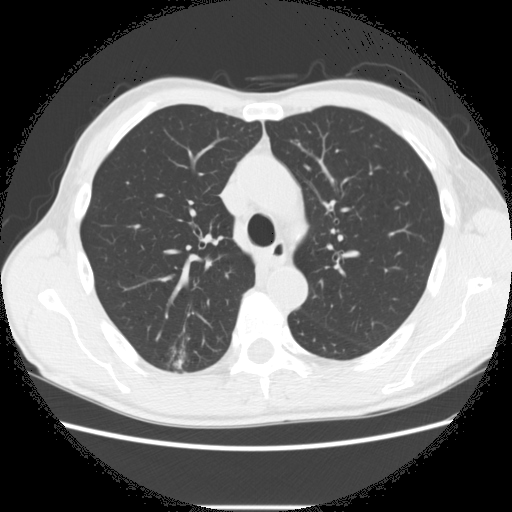
Low-dose screening chest CT, one axial slice. Position 197 of 282 along the scan axis. 120 kVp. Lung window (W 1500 / L -600 HU). 2.5 mm slice thickness. 512 × 512 image matrix.
Outlined on this slice (manually delineated by an expert):
- lesion 1 (tumor, upper lobe of right lung): bounding box <173,359,184,369> (left, top, right, bottom; pixels)